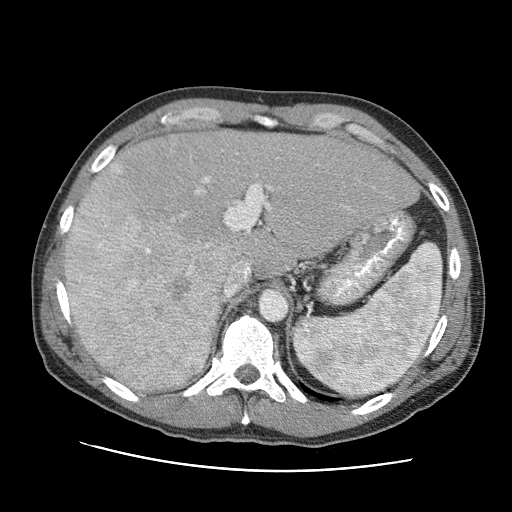
Contrast-enhanced abdominal CT (liver protocol), one axial slice; slice 64 of 95 in the series (ordered by position); 120 kVp; one of 2 acquisitions stored at this slice position; soft-tissue window (W 400 / L 40 HU); 512 × 512 image matrix, field of view 360 × 360 mm. From the clinical record (not read from this slice): diagnosis: hepatocellular carcinoma (patient treated with transarterial chemoembolisation; whether this scan precedes or follows treatment is not stated here); TNM stage (as recorded): Stage-IVA.
Structures marked on this image (semi-automatically segmented with operator editing):
- liver parenchyma outside the tumour (the mass and vessels are separate outlines, so this box may not span the whole liver): bounding box <64,130,418,390> (left, top, right, bottom; pixels)
- mass: <64,158,229,390>
- liver vessels: <112,165,375,368>